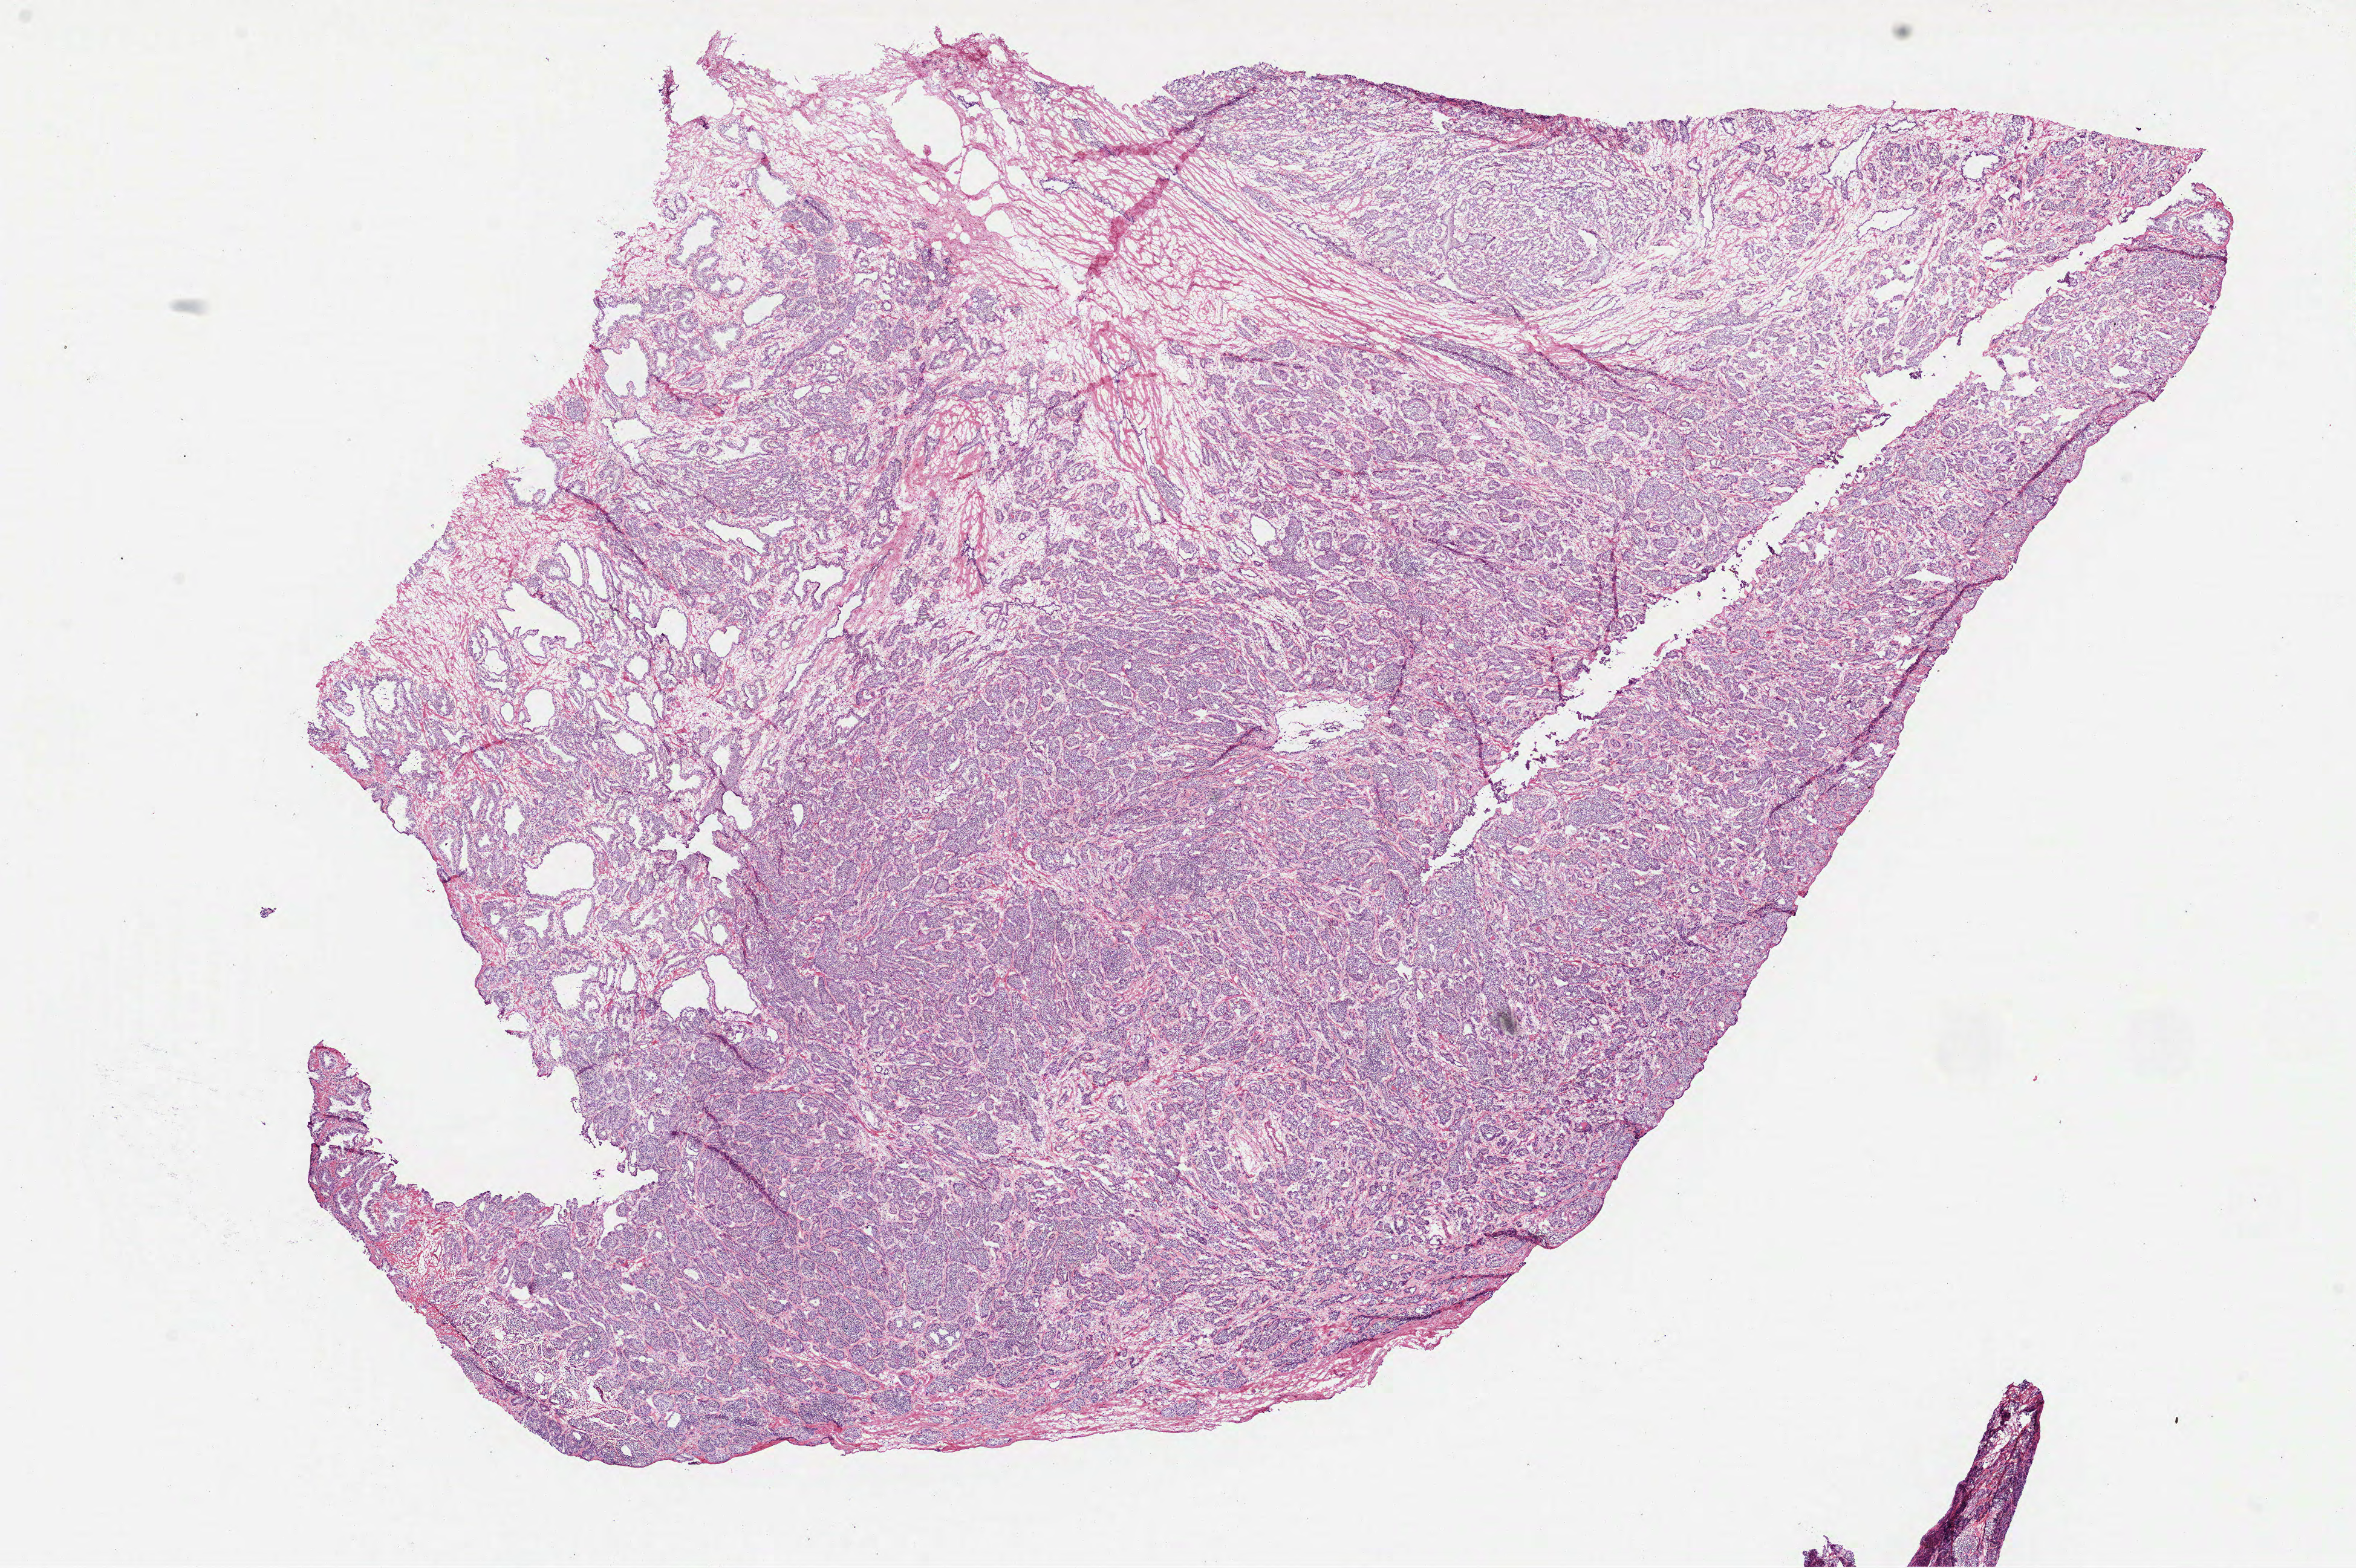
Digitized H&E tissue section (whole slide), low-resolution overview of the scanned area, about 15.7 x 10.5 mm (slide scanned at 40x). Frozen section. Primary tumour sample from the prostate. Patient: male, age at initial diagnosis 63 years. Gleason score: 7 (4+3). Composition of this section per pathologist review: tumour cells 90%, tumour nuclei 95%, normal cells 2%, stromal cells 8%, necrosis 0%. Infiltration values recorded for this section: lymphocyte infiltration 0%, monocyte infiltration 0%, neutrophil infiltration 0%.
Diagnosis: Acinar cell carcinoma (prostate gland). Laterality: bilateral.